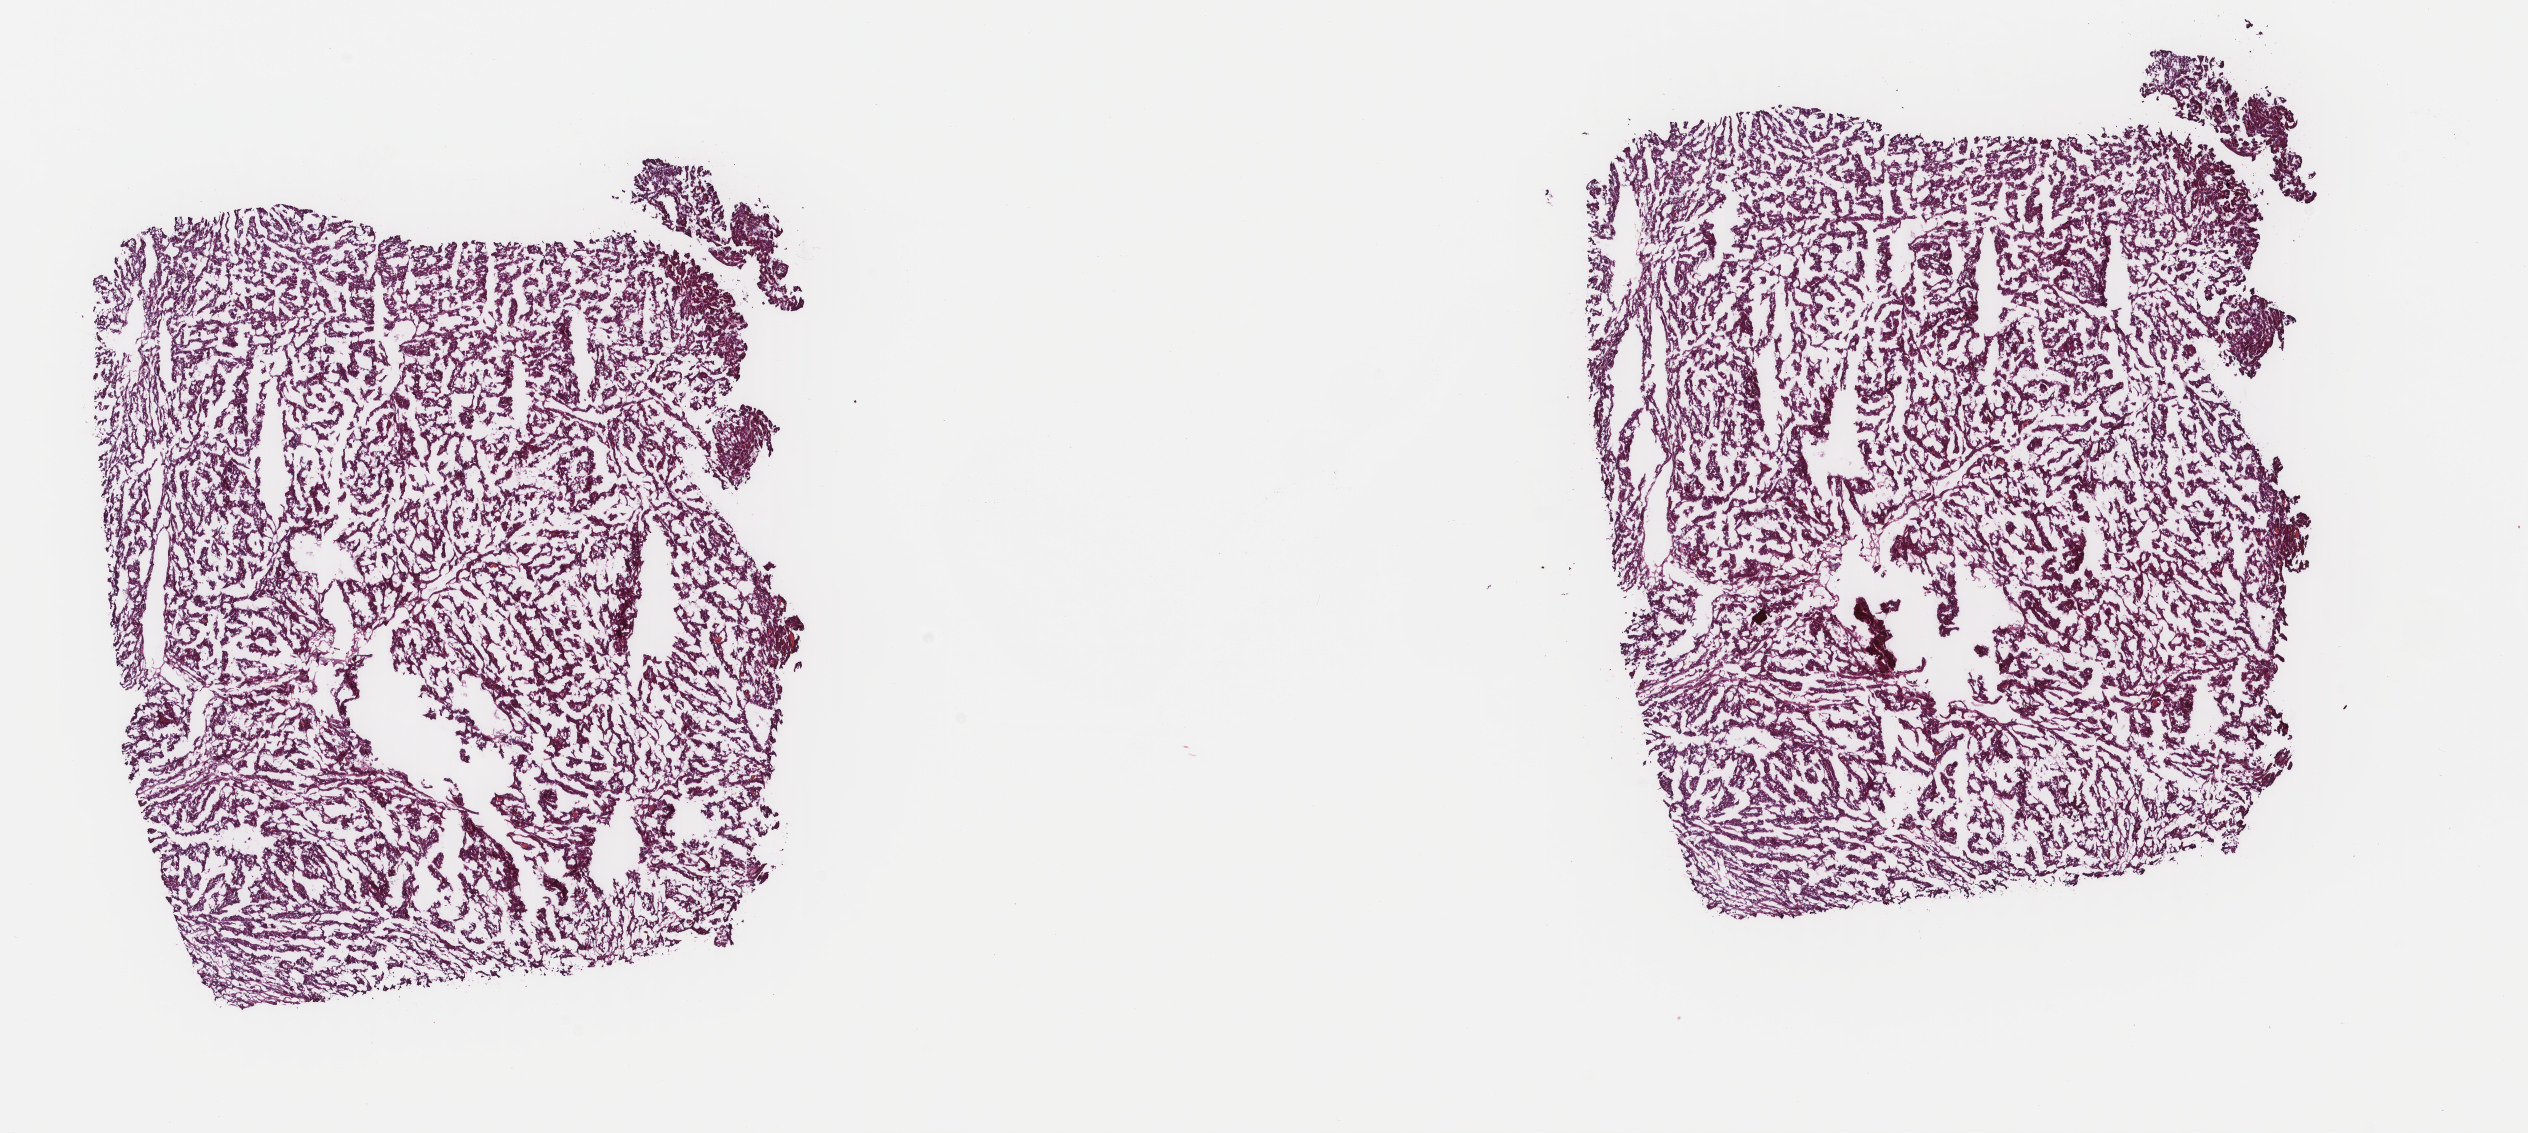
Whole-slide histology image, H&E, low-resolution overview of the scanned area, about 20.1 x 9.0 mm (acquisition: 40x scan). Frozen section from the top of the tissue portion. Liver, primary tumour sample. Male patient; age at initial diagnosis 45 years. Histologic grade: G2 (moderately differentiated). Pathologist review of this section (percent, as recorded): tumour cells 100%, tumour nuclei 97%, normal cells 0%, stromal cells 0%, necrosis 0%. Inflammatory infiltration, as recorded: lymphocyte infiltration 0%, monocyte infiltration 0%, neutrophil infiltration 0%.
TNM: T1 N0 M0. AJCC pathologic stage: I (5th edition). Diagnosis: Hepatocellular carcinoma, NOS.